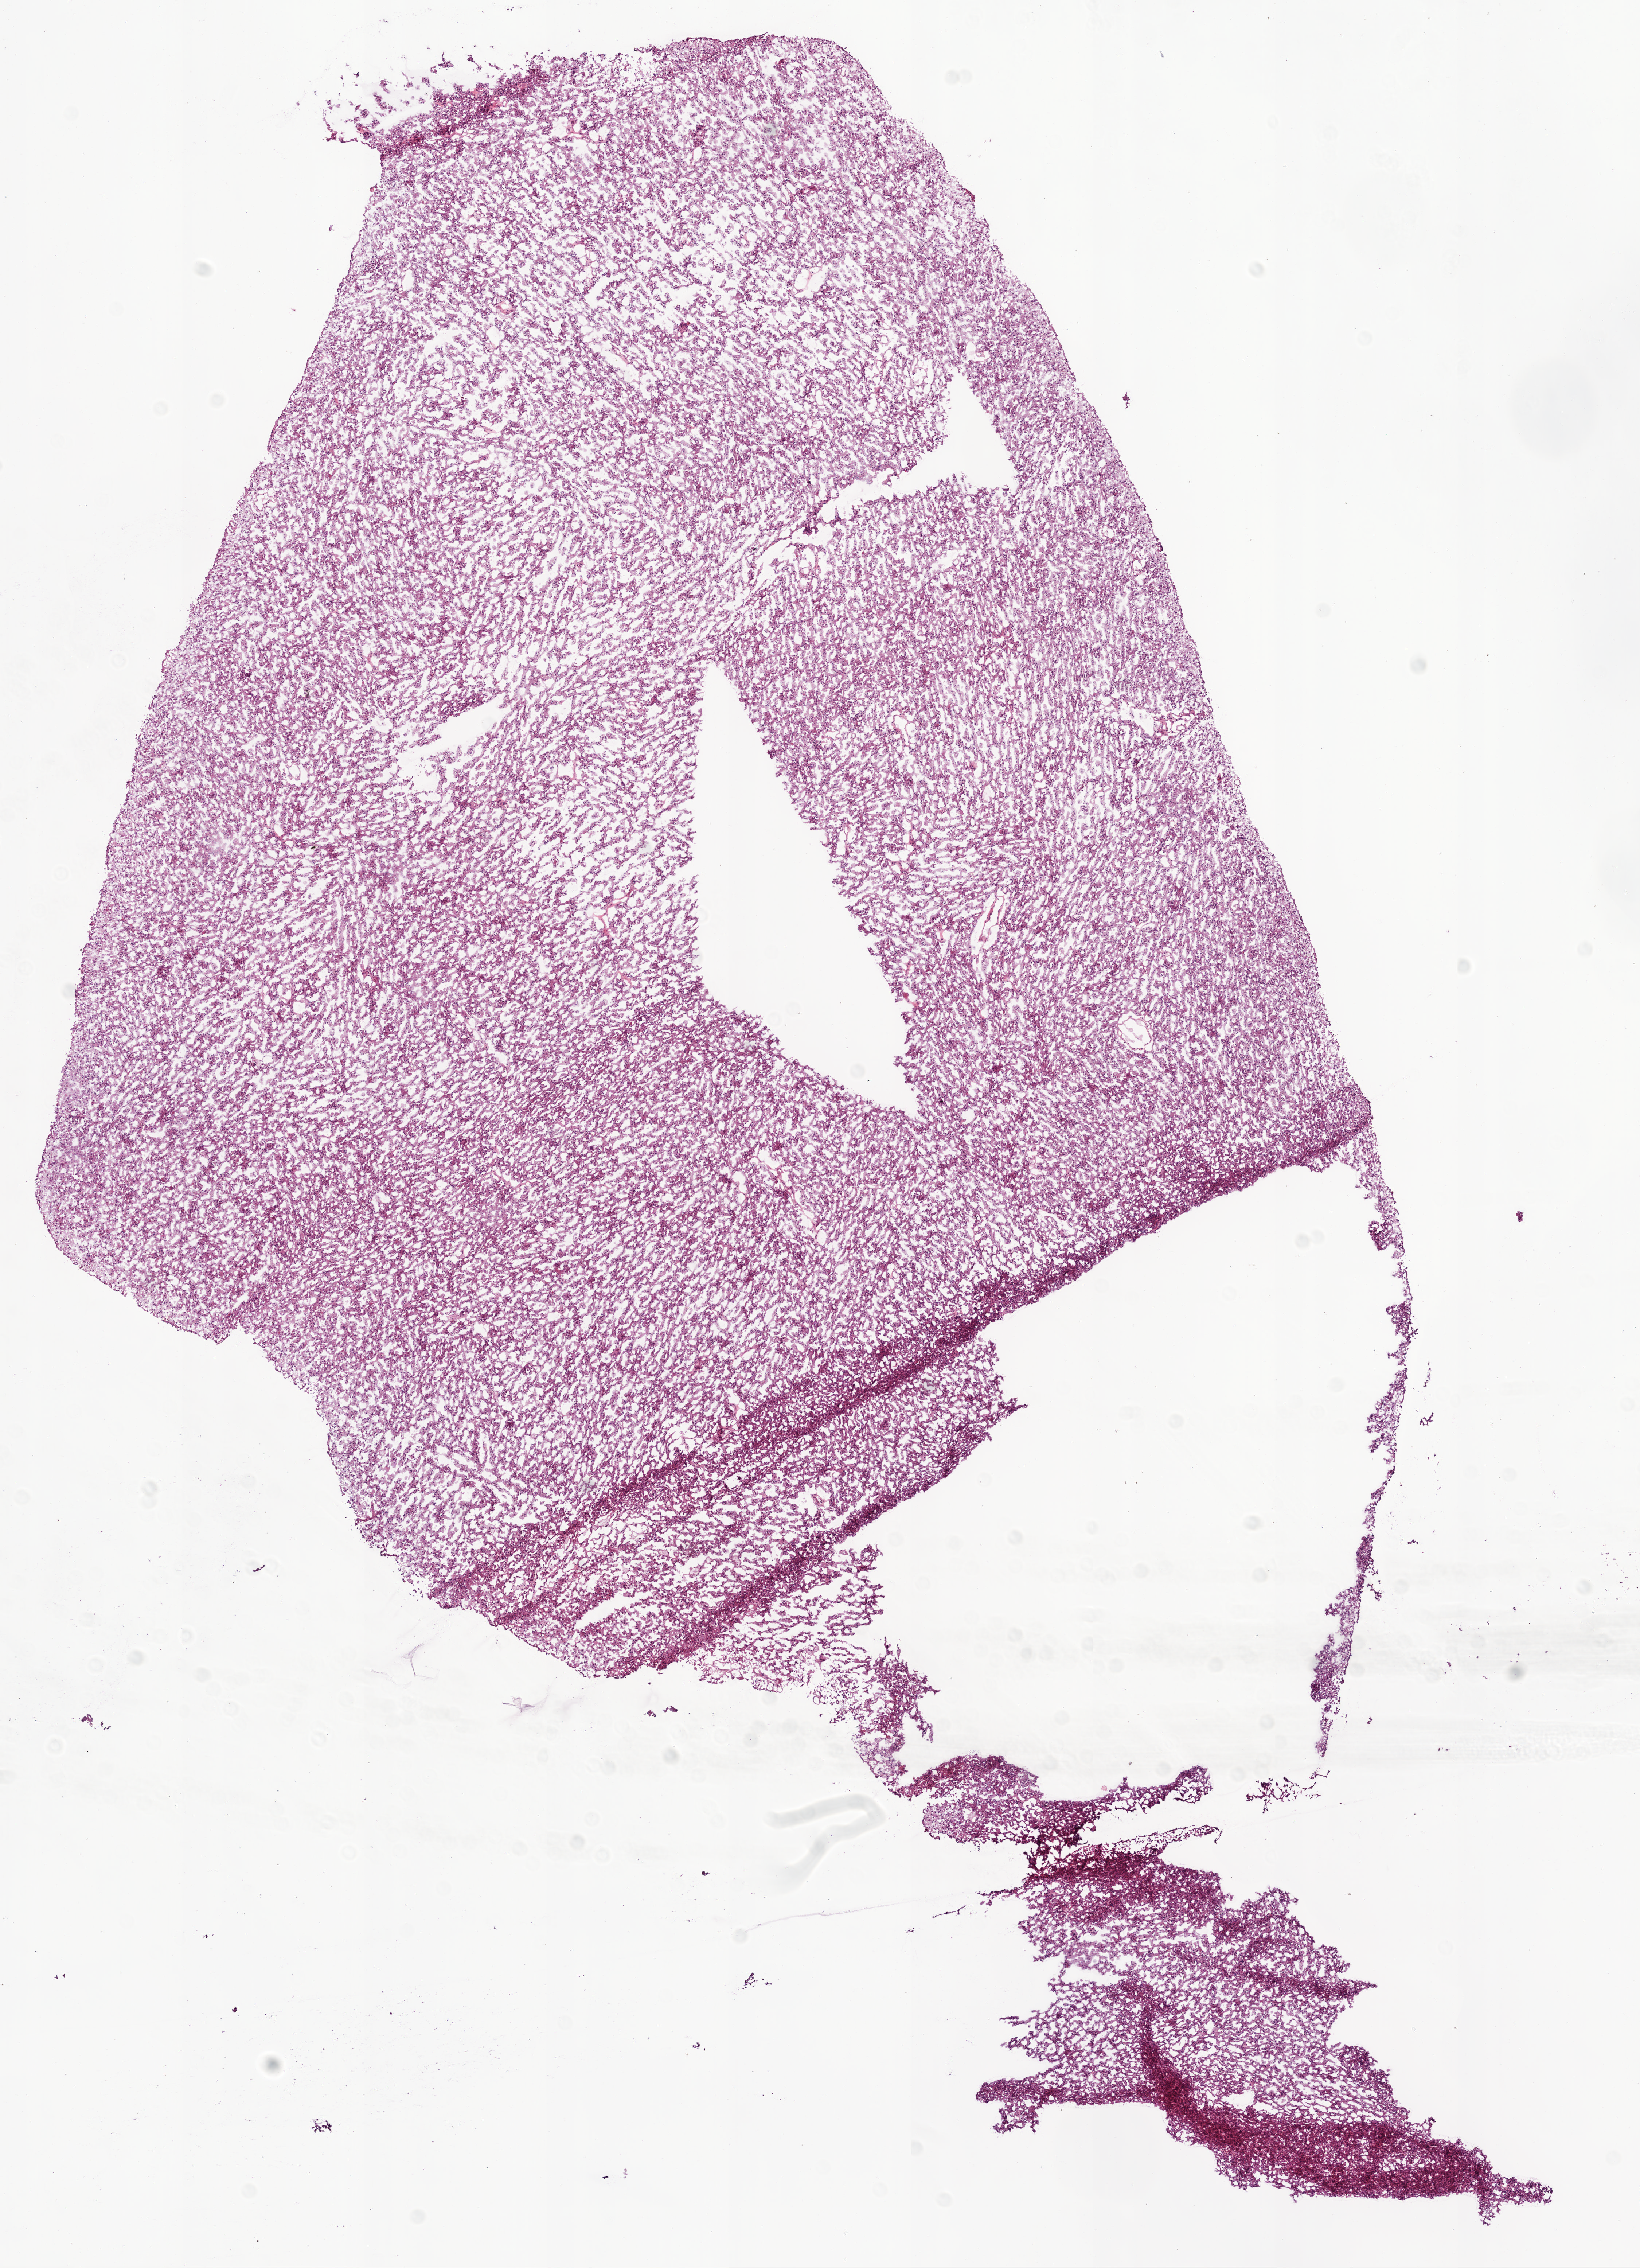
Digitized H&E tissue section (whole slide) — low-resolution overview of the scanned area, about 9.0 x 12.5 mm (acquisition: 20x scan), frozen section from the bottom of the tissue portion, primary tumour sample from the brain. Female, age 75 years at initial diagnosis. Composition of this section per pathologist review: tumour cells 95%, tumour nuclei 90%, normal cells 0%, stromal cells 5%, necrosis 0%.
• histologic diagnosis: Glioblastoma